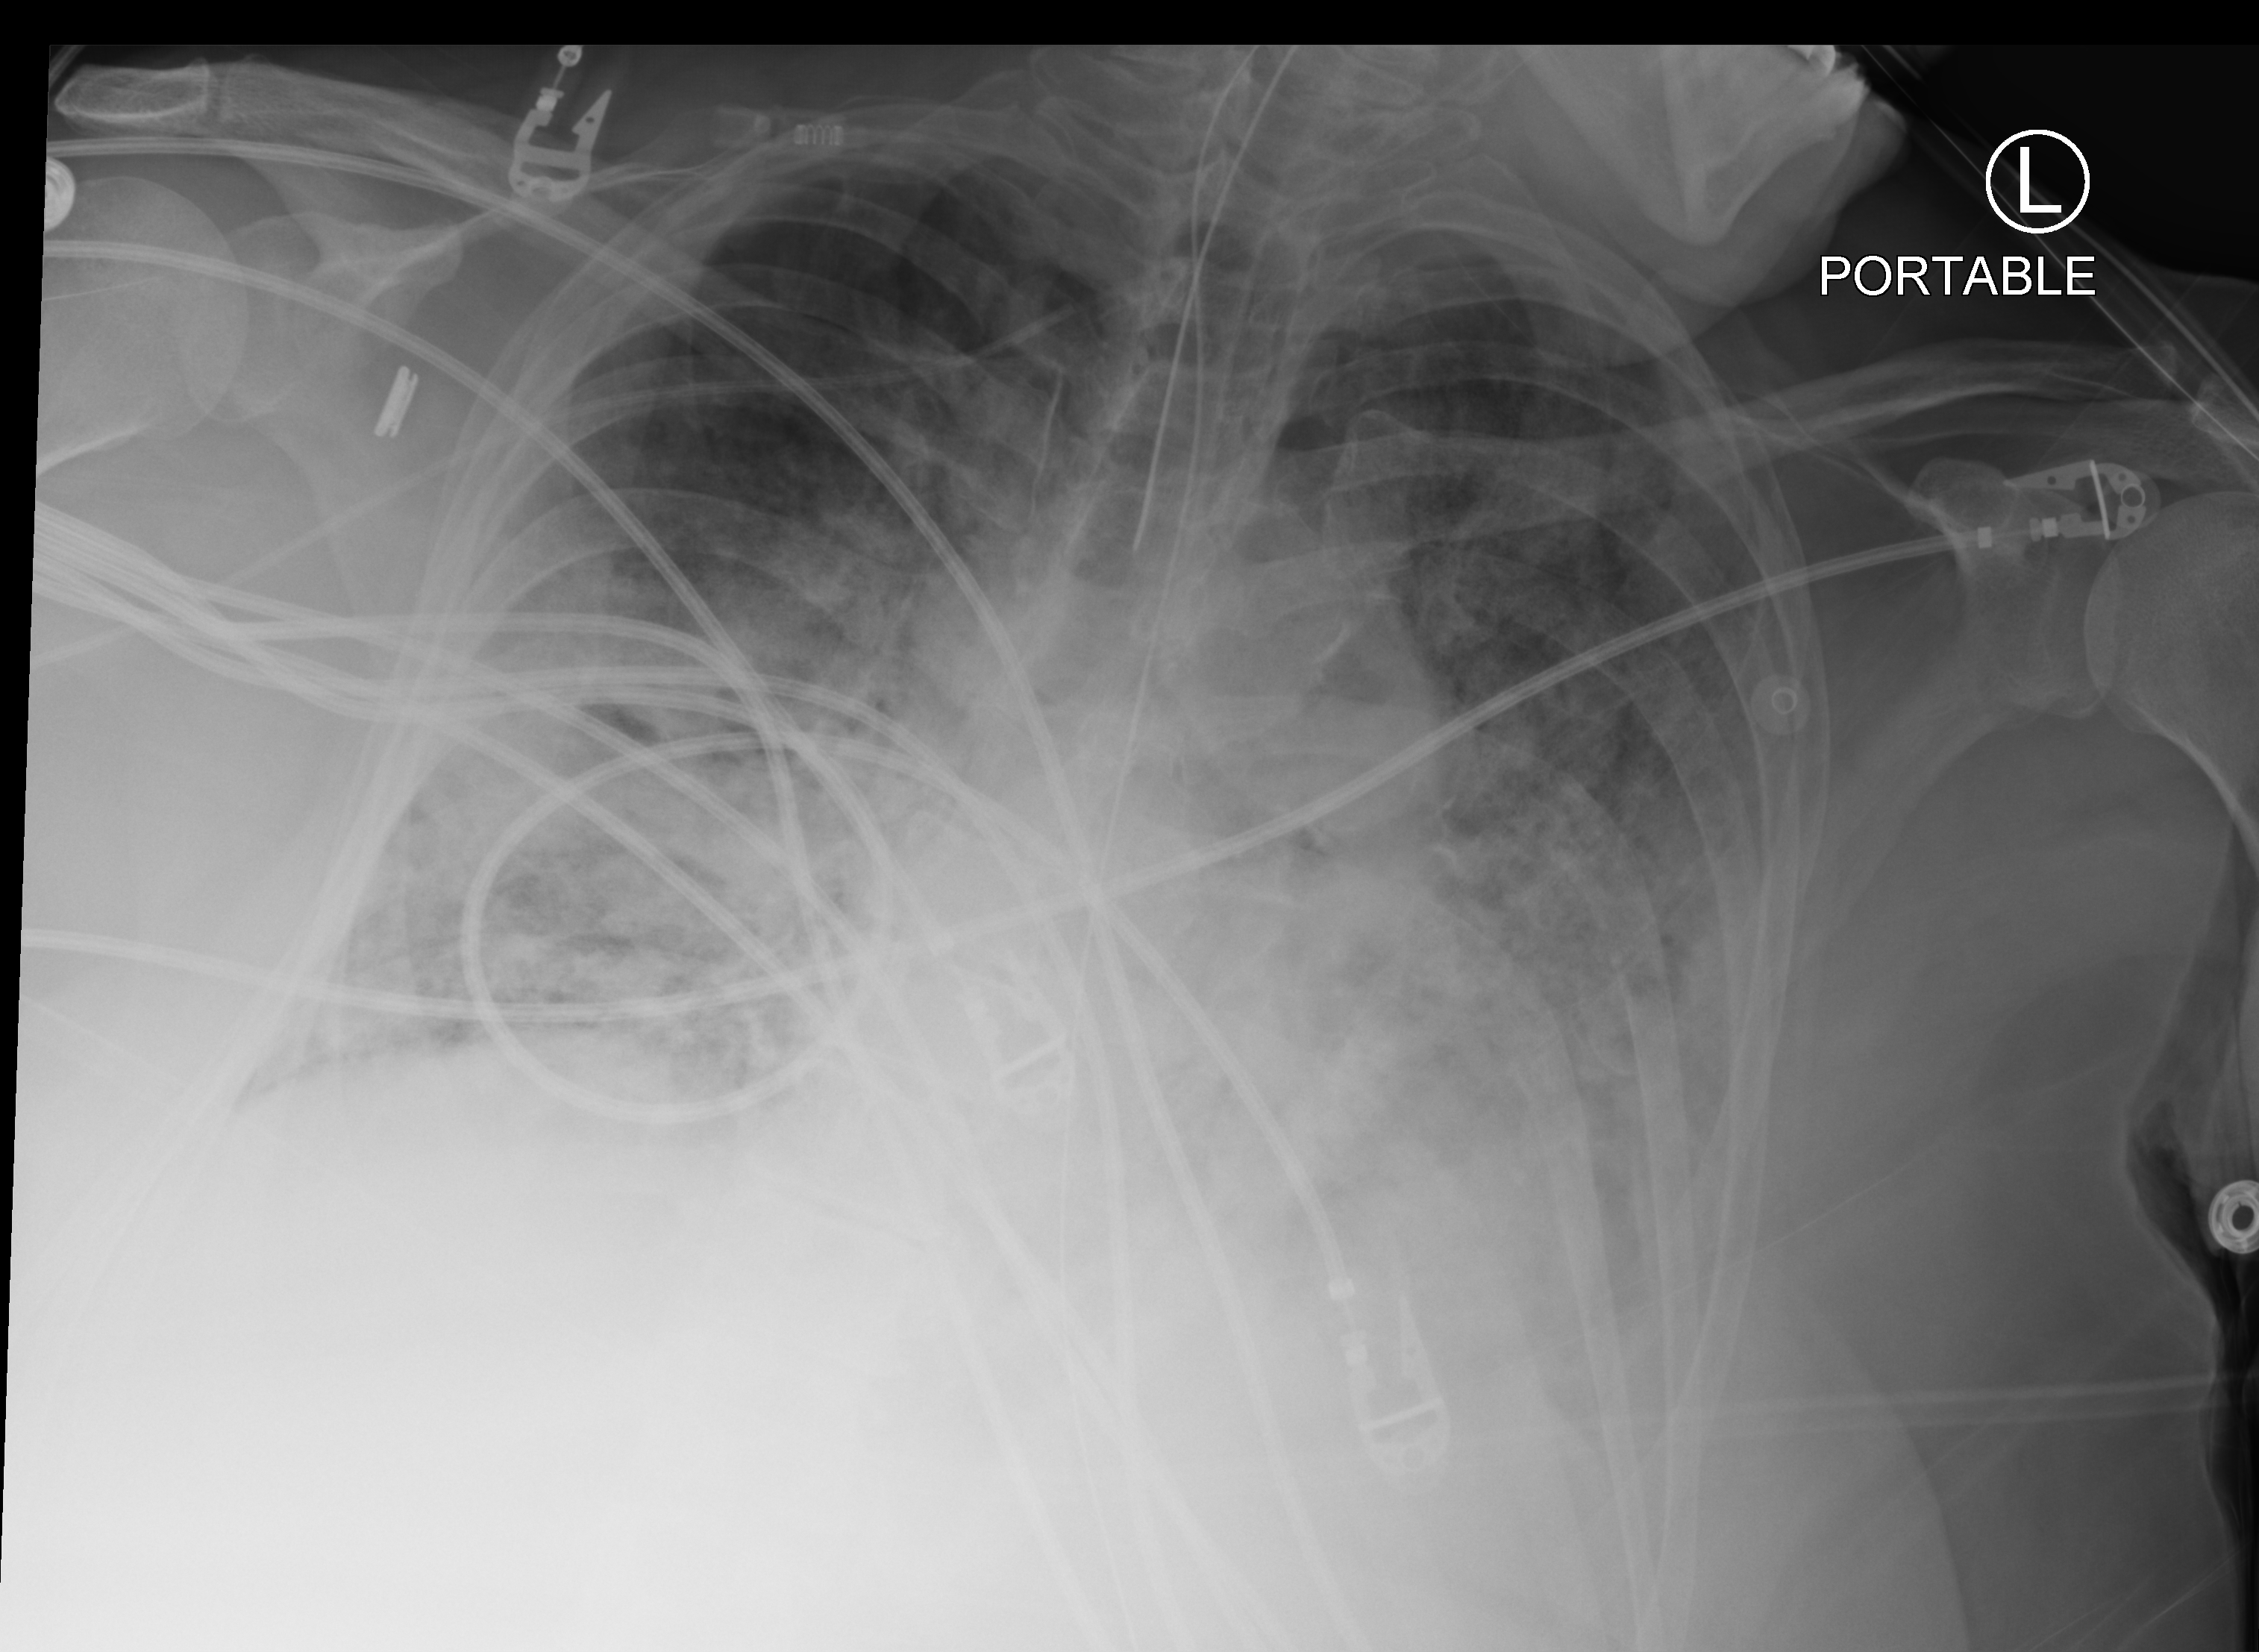
Portable chest radiograph, anteroposterior (AP) projection. Female patient hospitalised with COVID-19, age 60–74 years.
Hospital-stay facts (about this admission, not read from this image; timing relative to this image not recorded): mechanically ventilated during this hospital stay: yes; diabetes (admission record): no.